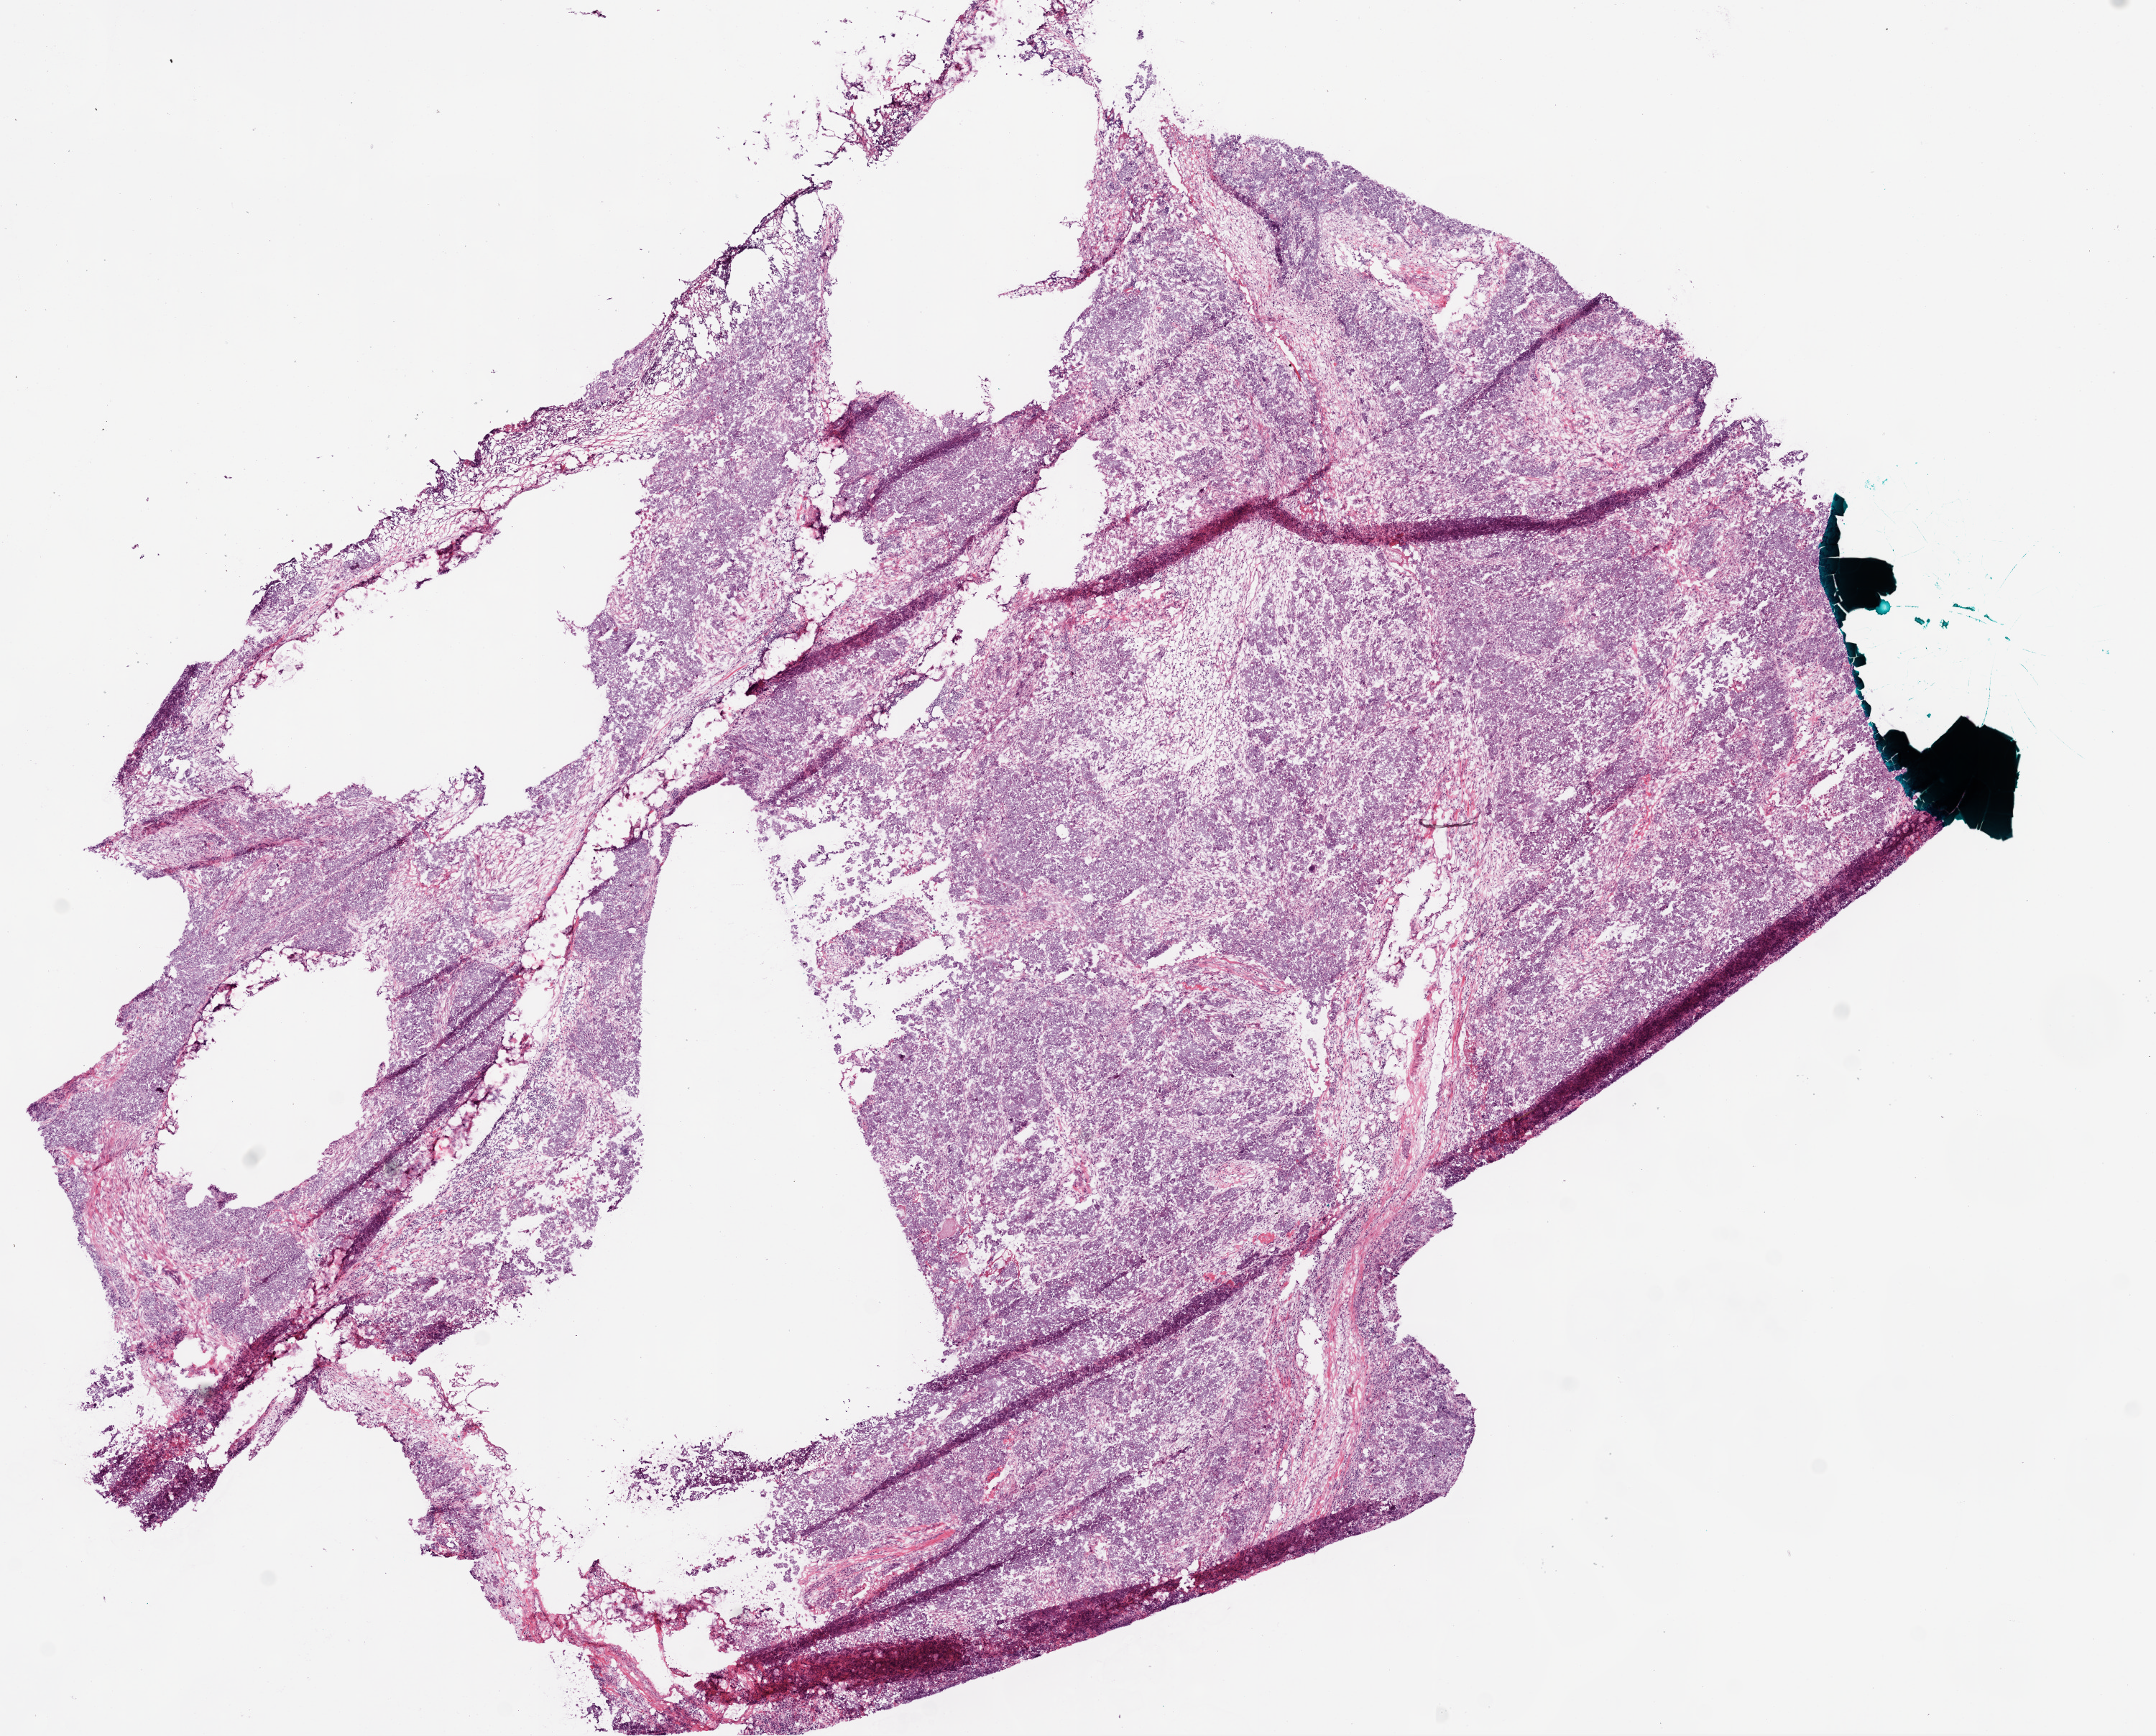
Whole-slide histology image, H&E — whole scanned area (about 12.0 x 9.7 mm) shown as a low-resolution overview. Frozen section. Sample: primary tumour, ovary. Female patient; age at initial diagnosis 68 years. Histologic grade: G3 (poorly differentiated). Composition of this section per pathologist review: tumour cells 85%, tumour nuclei 70%, normal cells 10%, stromal cells 0%, necrosis 5%.
FIGO stage: IIIC. Pathologic diagnosis: Serous cystadenocarcinoma, NOS. Laterality: bilateral.